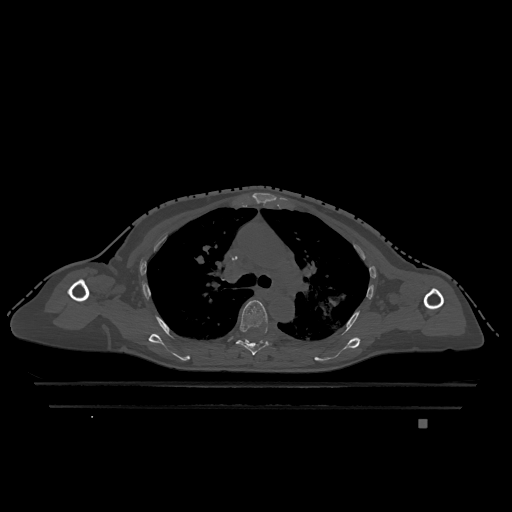
CT including the spine, one axial slice. Slice 833 of 1317 in the series (ordered by position). Bone window (W 1800 / L 400 HU). 0.5 mm slice thickness. 512 × 512 image matrix, field of view 500 × 500 mm. Patient: female, 74 years. Case-level facts recorded for this patient, not image findings: primary cancer: lung; vertebrae with lytic lesions (as recorded): T1, T4, T5, T6, L4, L5.
Annotated regions visible in this slice (semi-automatically segmented with operator editing):
- T5 vertebra: bounding box (x1, y1, x2, y2) in pixels: (236, 300, 272, 355)